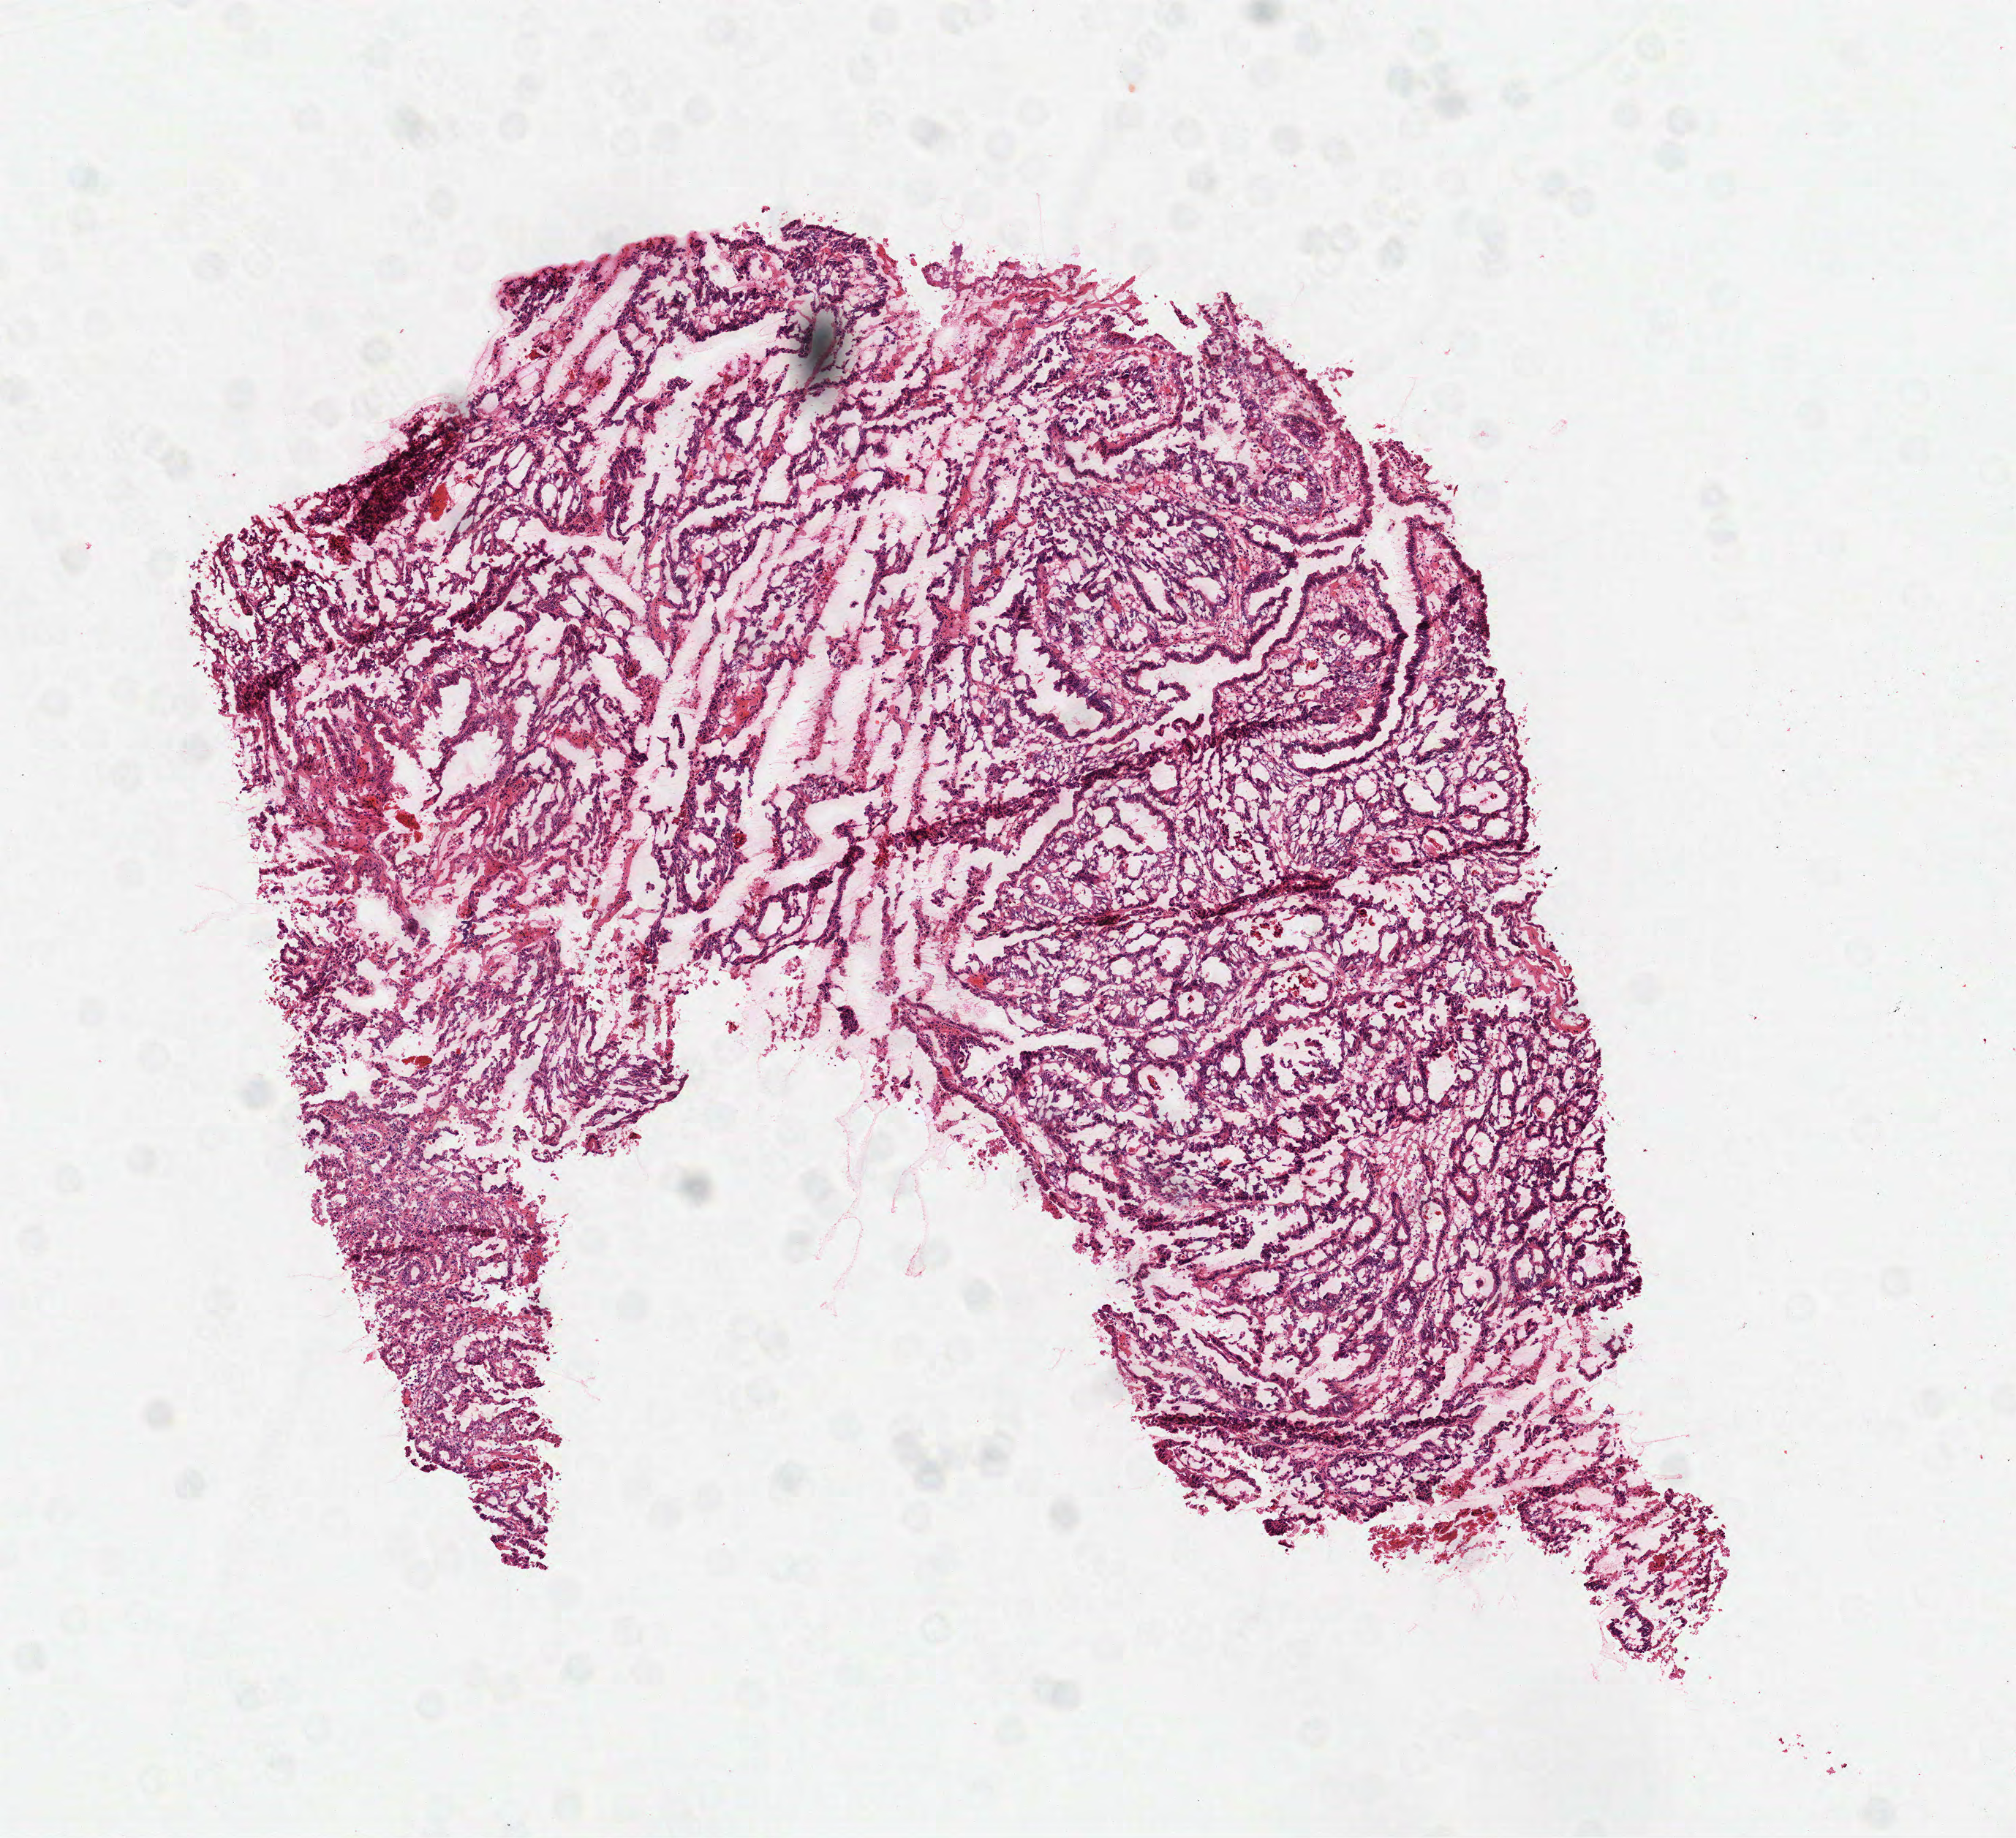
Whole-slide histology image, H&E, whole scanned area (about 5.6 x 5.1 mm, slide scanned at 40x) shown as a low-resolution overview. Frozen section from the top of the tissue portion. Rectum, primary tumour sample. Female patient. Pathologist review of this section (percent, as recorded): tumour cells 83%, tumour nuclei 80%, normal cells 5%, stromal cells 5%, necrosis 7%.
Pathologic diagnosis: Adenocarcinoma, NOS. AJCC pathologic stage: IIA (6th edition).